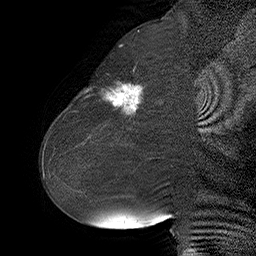
Breast MRI (dynamic contrast-enhanced), one sagittal slice. Position 24 of 55 along the scan axis. Dynamic contrast-enhanced series, time point 2 of 6 at this slice position (early post-contrast). 1.5 T. TE 4.5 ms, TR 32.4 ms. 256 × 256 image matrix, field of view 180 × 180 mm. Female patient. From the clinical record (not read from this slice): setting: breast cancer imaged before/during neoadjuvant chemotherapy; receptor status: HER2-positive.
Outlined on this slice (semi-automatically segmented with operator editing):
- analysis volume of interest (the breast-tissue region the enhancement analysis was run in; not a lesion): bounding box <80,64,163,134> (left, top, right, bottom; pixels)
- tumour enhancement mask (voxels above the 100 % enhancement threshold inside the analysis volume of interest): <85,83,142,115>